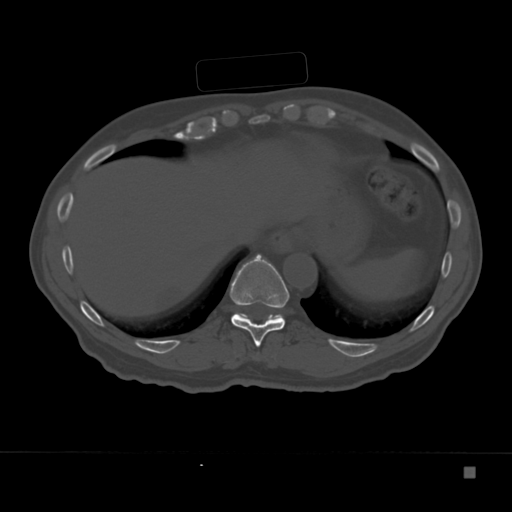
CT including the spine, one axial slice. Position 169 of 332 along the scan axis. Reconstruction kernel Br40s. 120 kVp. Bone window (W 1800 / L 400 HU). 1.5 mm slice thickness. 512 × 512 image matrix. Patient: male, 72 years. Case-level facts recorded for this patient, not image findings: primary cancer: skeletal.
Annotated regions visible in this slice (semi-automatically segmented with operator editing):
- T10 vertebra: bounding box [x1, y1, x2, y2] px = [230, 254, 290, 347]
- T11 vertebra: [235, 312, 283, 320]